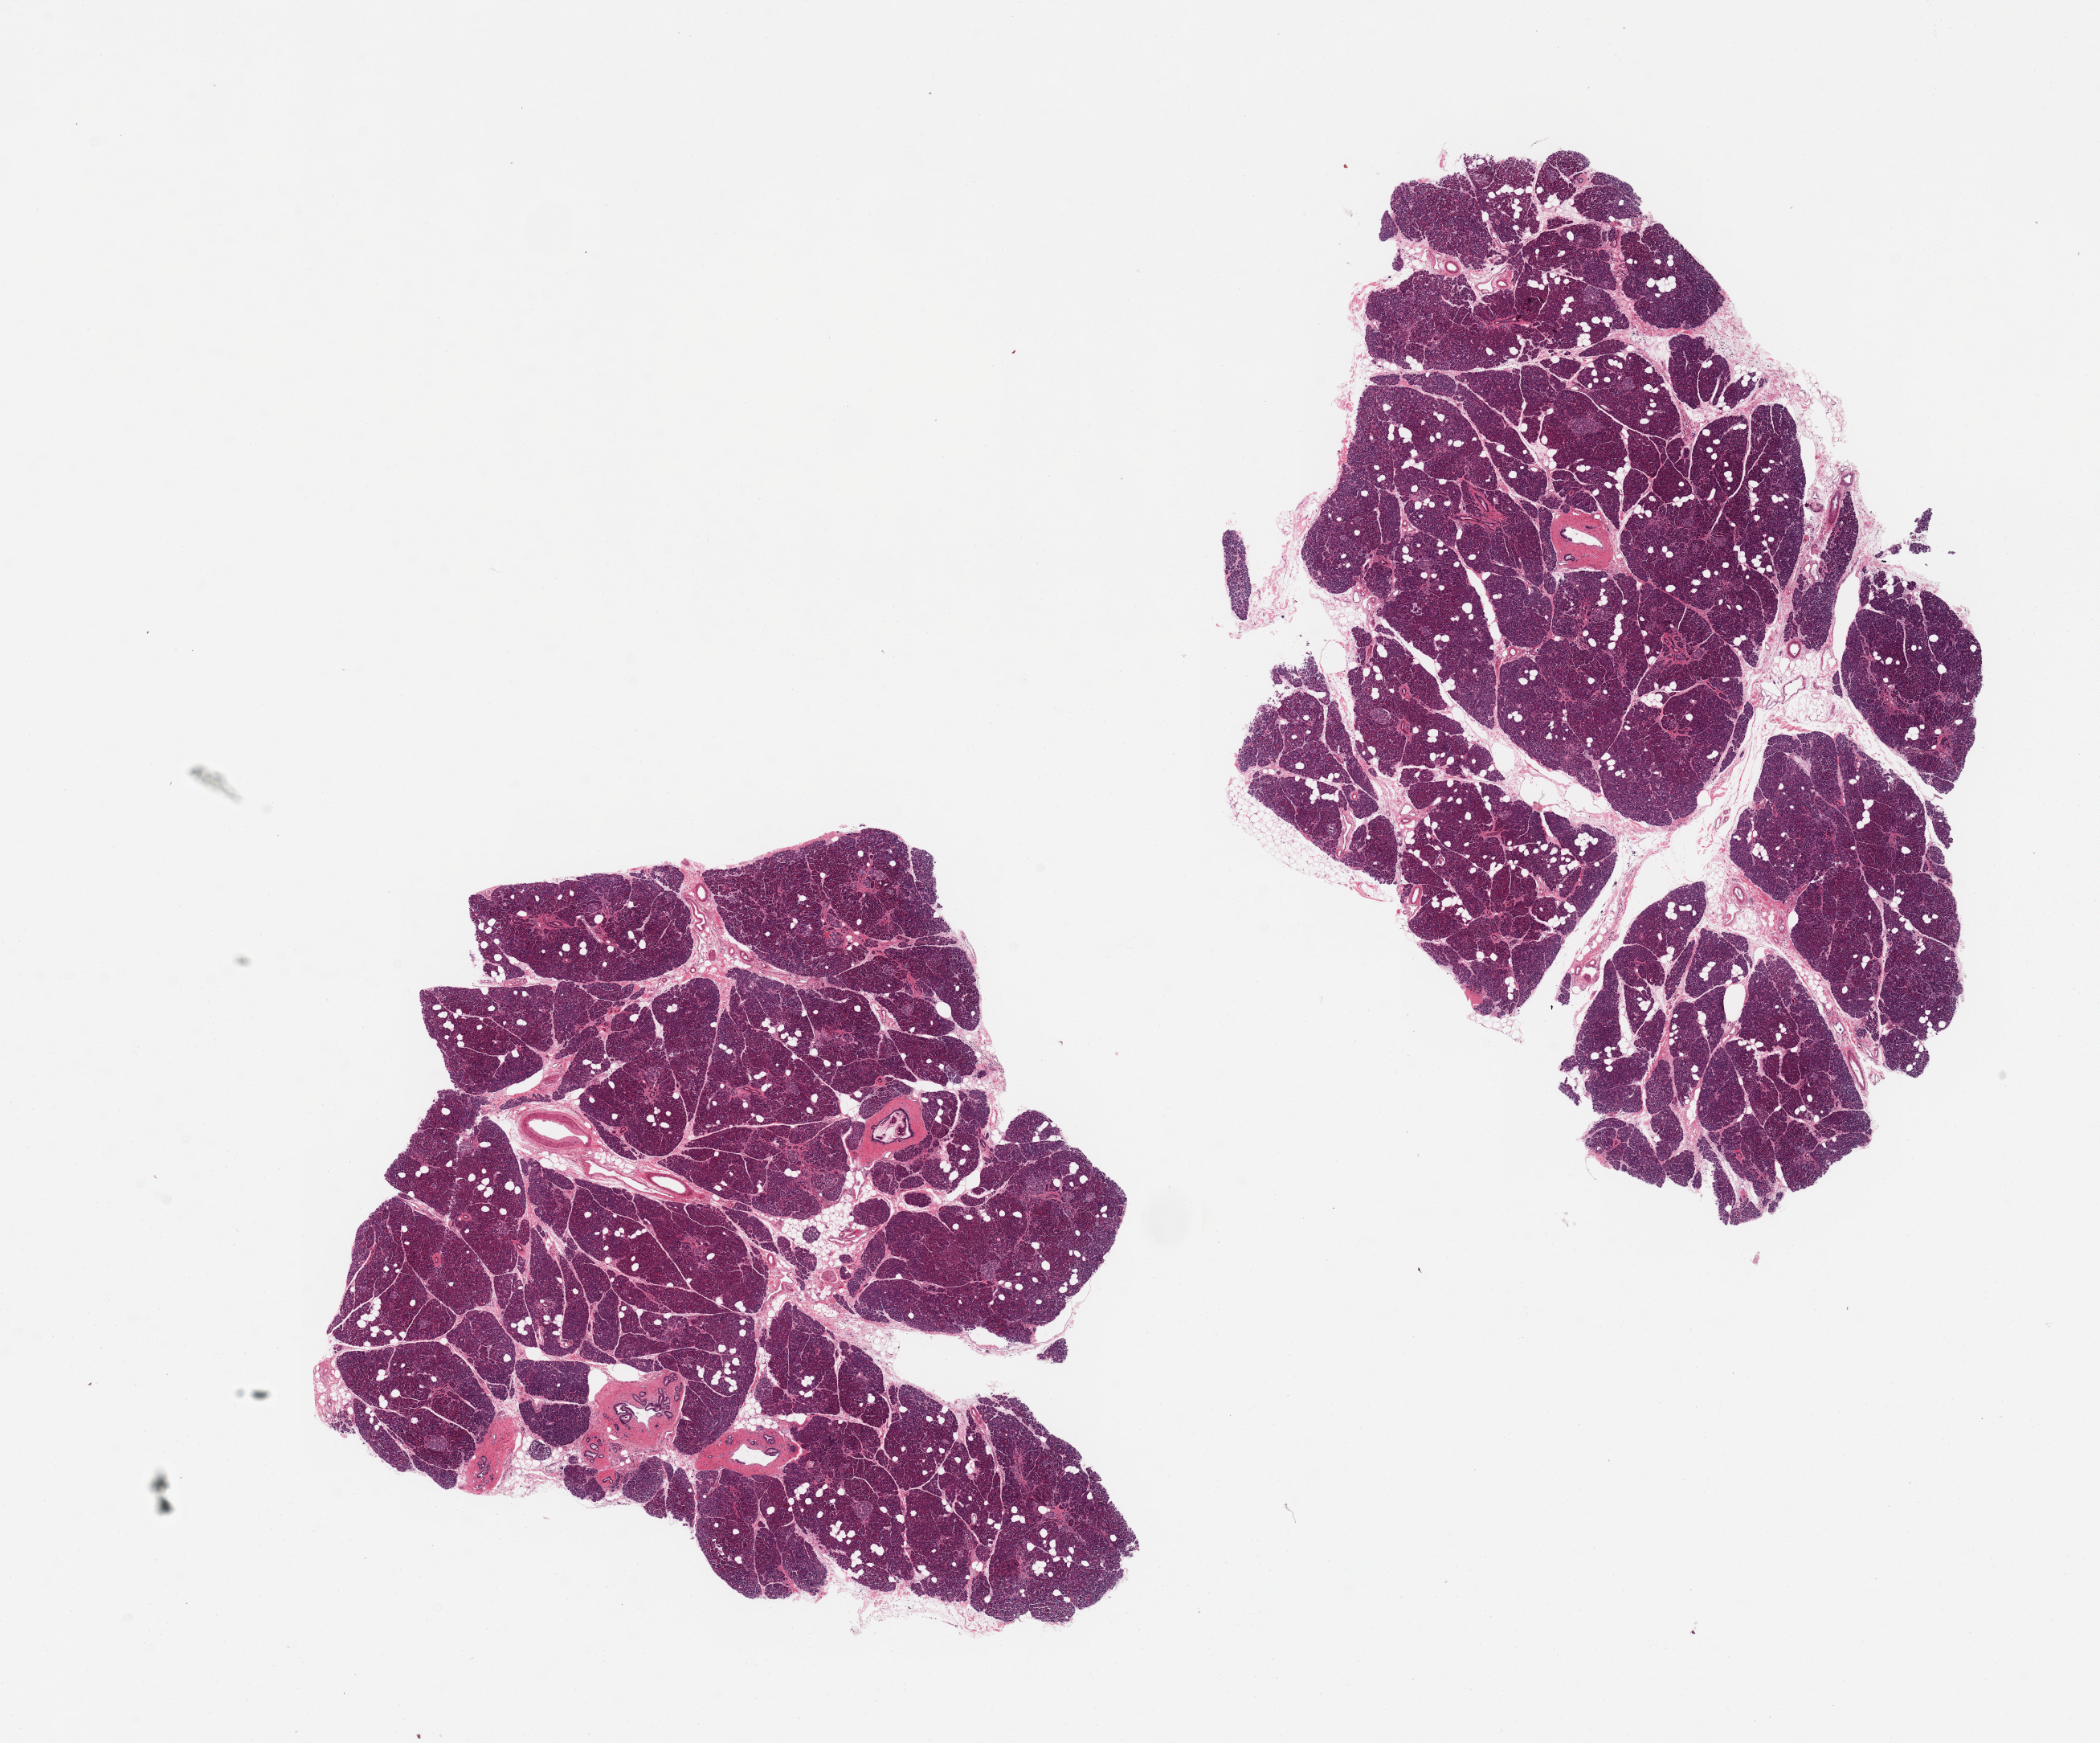
H&E whole-slide image, brightfield, whole scanned area (about 20.7 x 17.2 mm) shown as a low-resolution overview; PAXgene-fixed paraffin-embedded (PFPE) section; target tissue: pancreas; donor tissue sample. Donor sex: female.
• review note (as recorded): 2 pieces